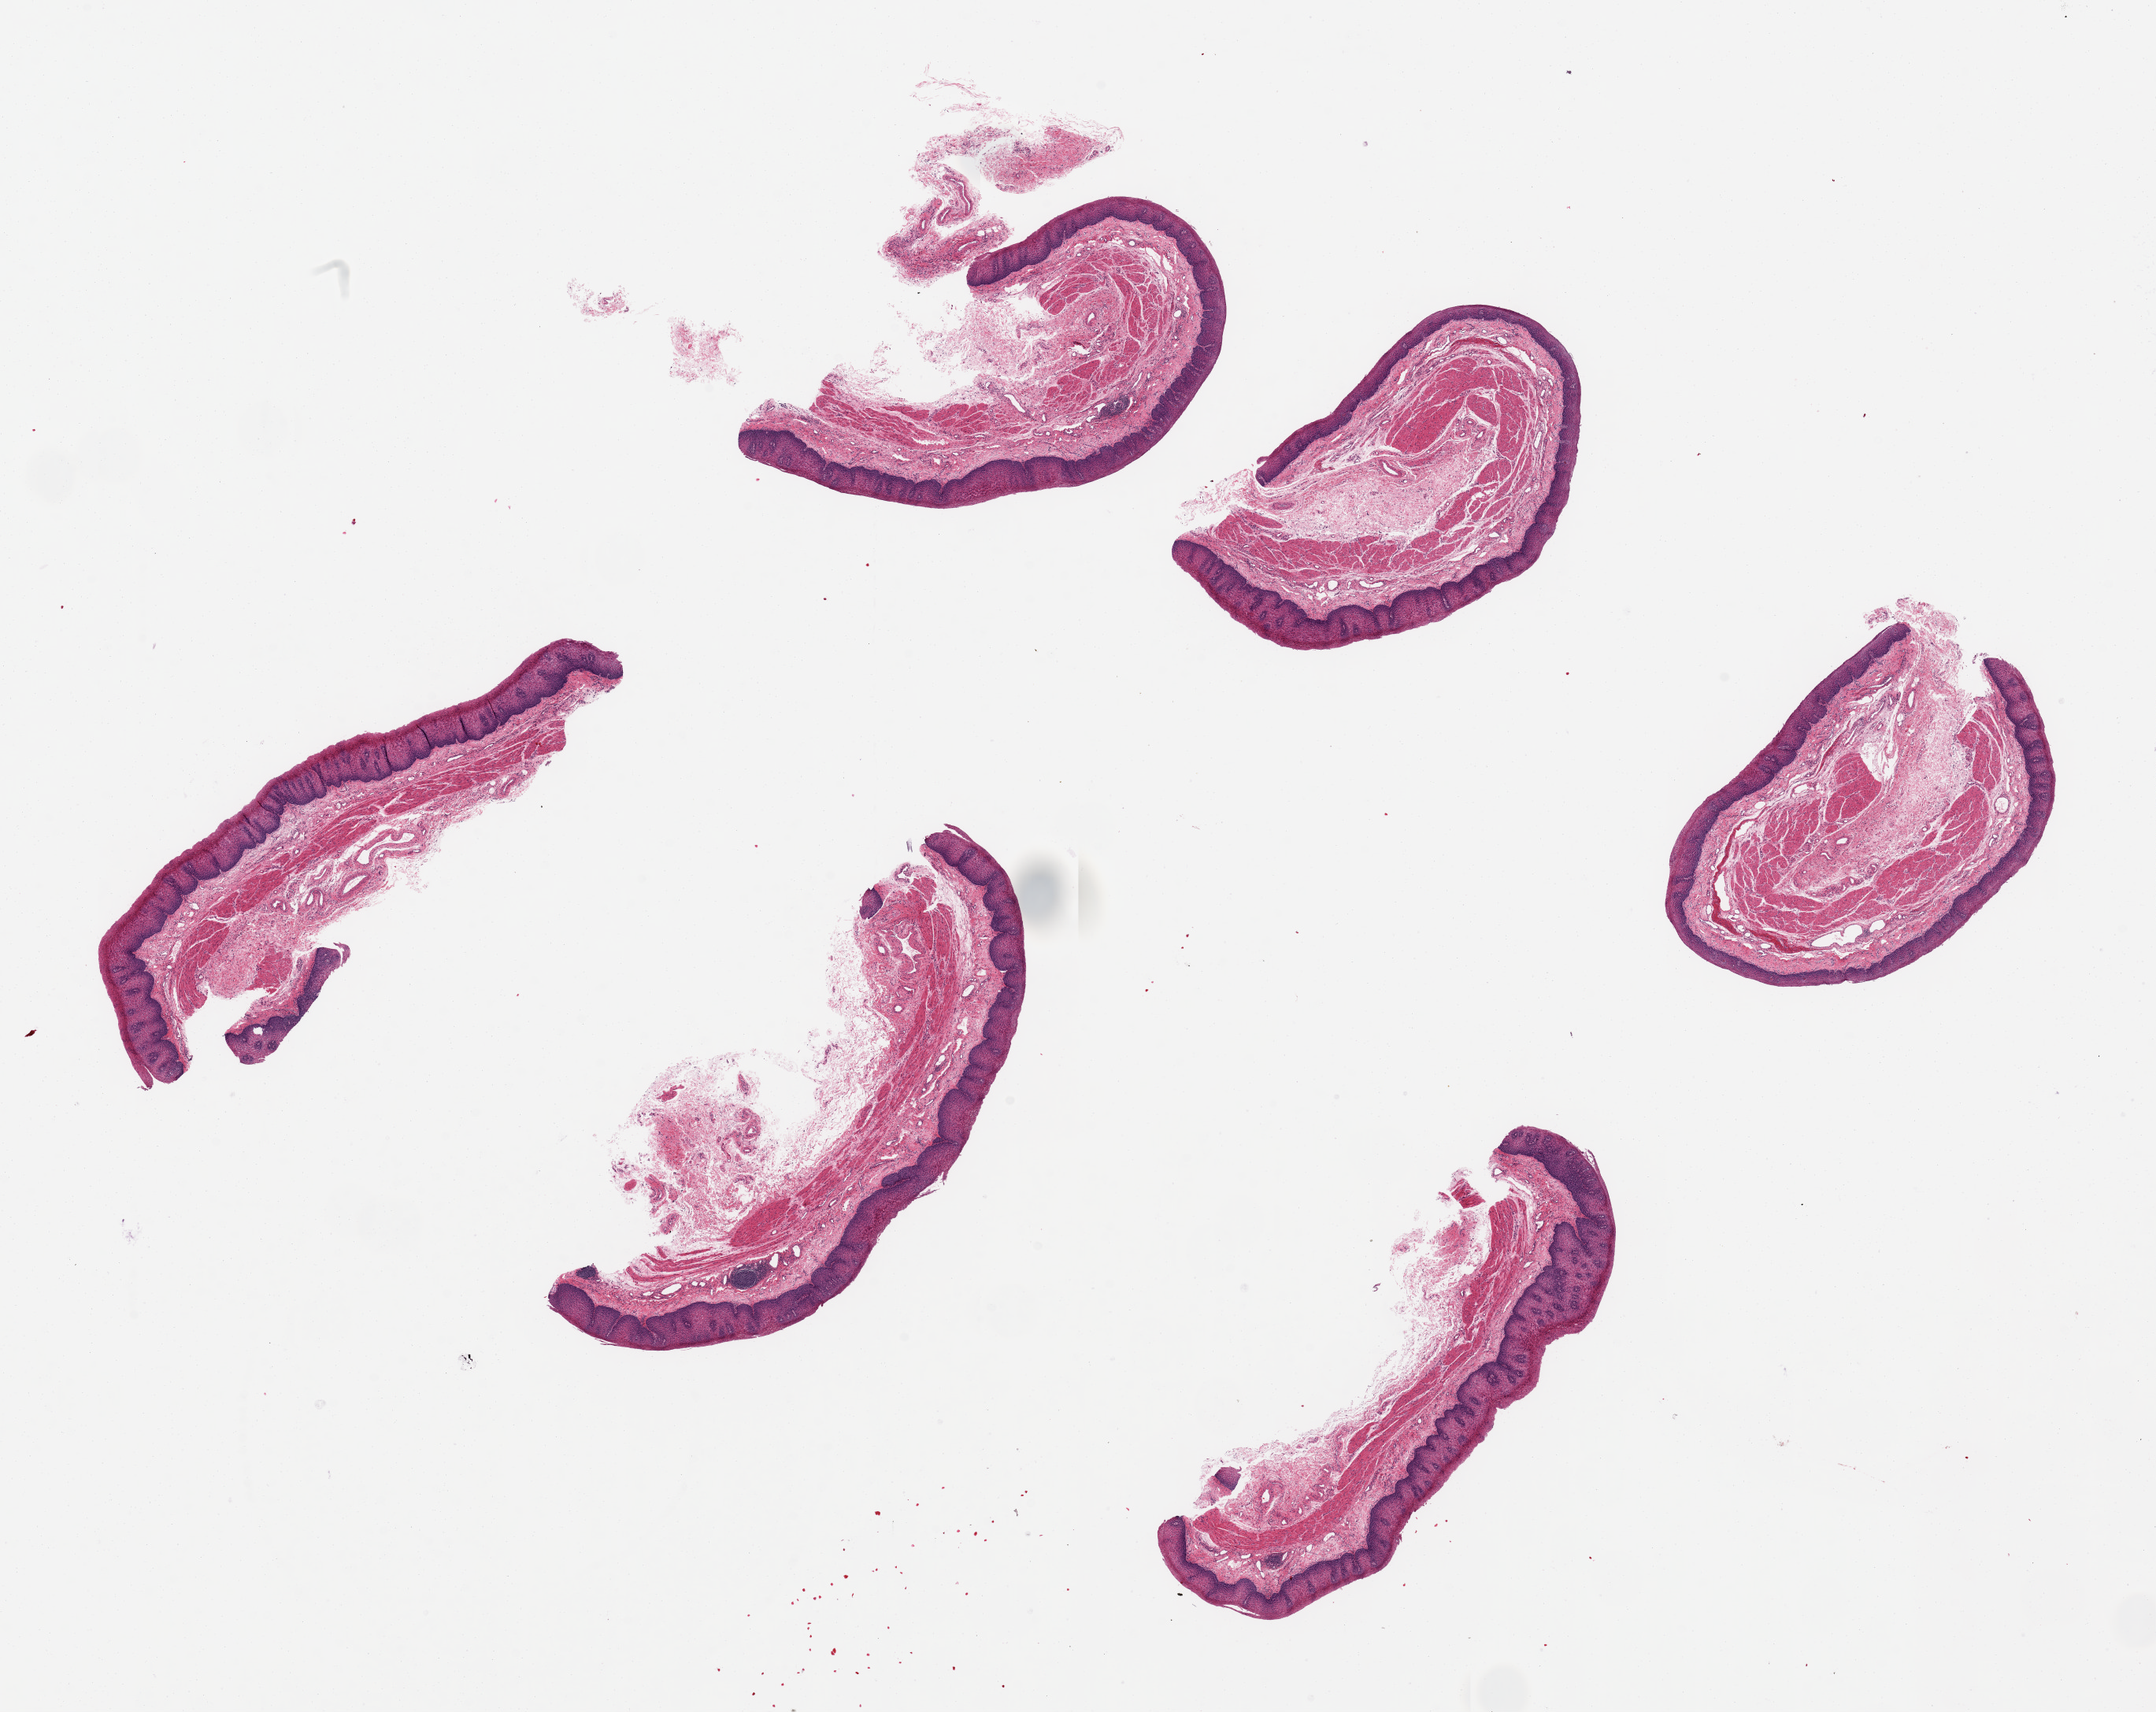
Hematoxylin and eosin (H&E) whole-slide image, whole scanned area (about 21.7 x 17.2 mm) shown as a low-resolution overview, PAXgene-fixed paraffin-embedded (PFPE) section, target tissue: esophageal mucous membrane, donor tissue sample. Donor sex: male.
Reviewer comment on this tissue sample: 6 pieces, 6x1.5mm. Squamous mucosa is ~20-30% of thickness.